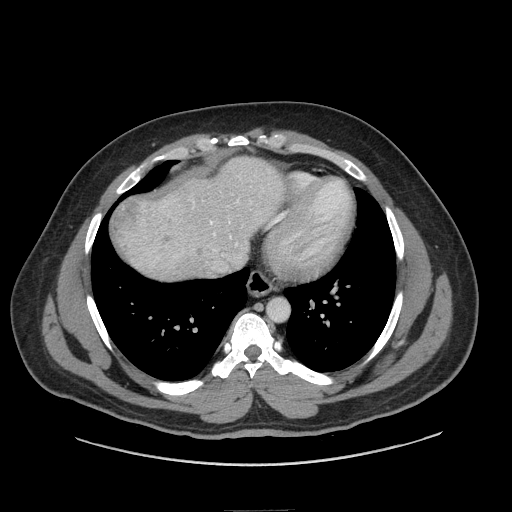
Contrast-enhanced abdominal CT (liver protocol), one axial slice; slice 73 of 87 in the series (ordered by position); 140 kVp; soft-tissue window (W 400 / L 40 HU); 2.5 mm slice thickness; 512 × 512 image matrix, field of view 440 × 440 mm. Case-level facts recorded for this patient, not image findings: diagnosis: hepatocellular carcinoma (patient treated with transarterial chemoembolisation; whether this scan precedes or follows treatment is not stated here); TNM stage (as recorded): Stage-II.
Annotated regions visible in this slice (semi-automatic segmentation, software-assisted and operator-edited):
- abdominal aorta: bounding box [x1, y1, x2, y2] px = [268, 300, 288, 321]
- liver parenchyma outside the tumour (the mass and vessels are separate outlines, so this box may not span the whole liver): [116, 158, 276, 278]
- mass: [111, 198, 177, 255]
- liver vessels: [210, 200, 239, 245]